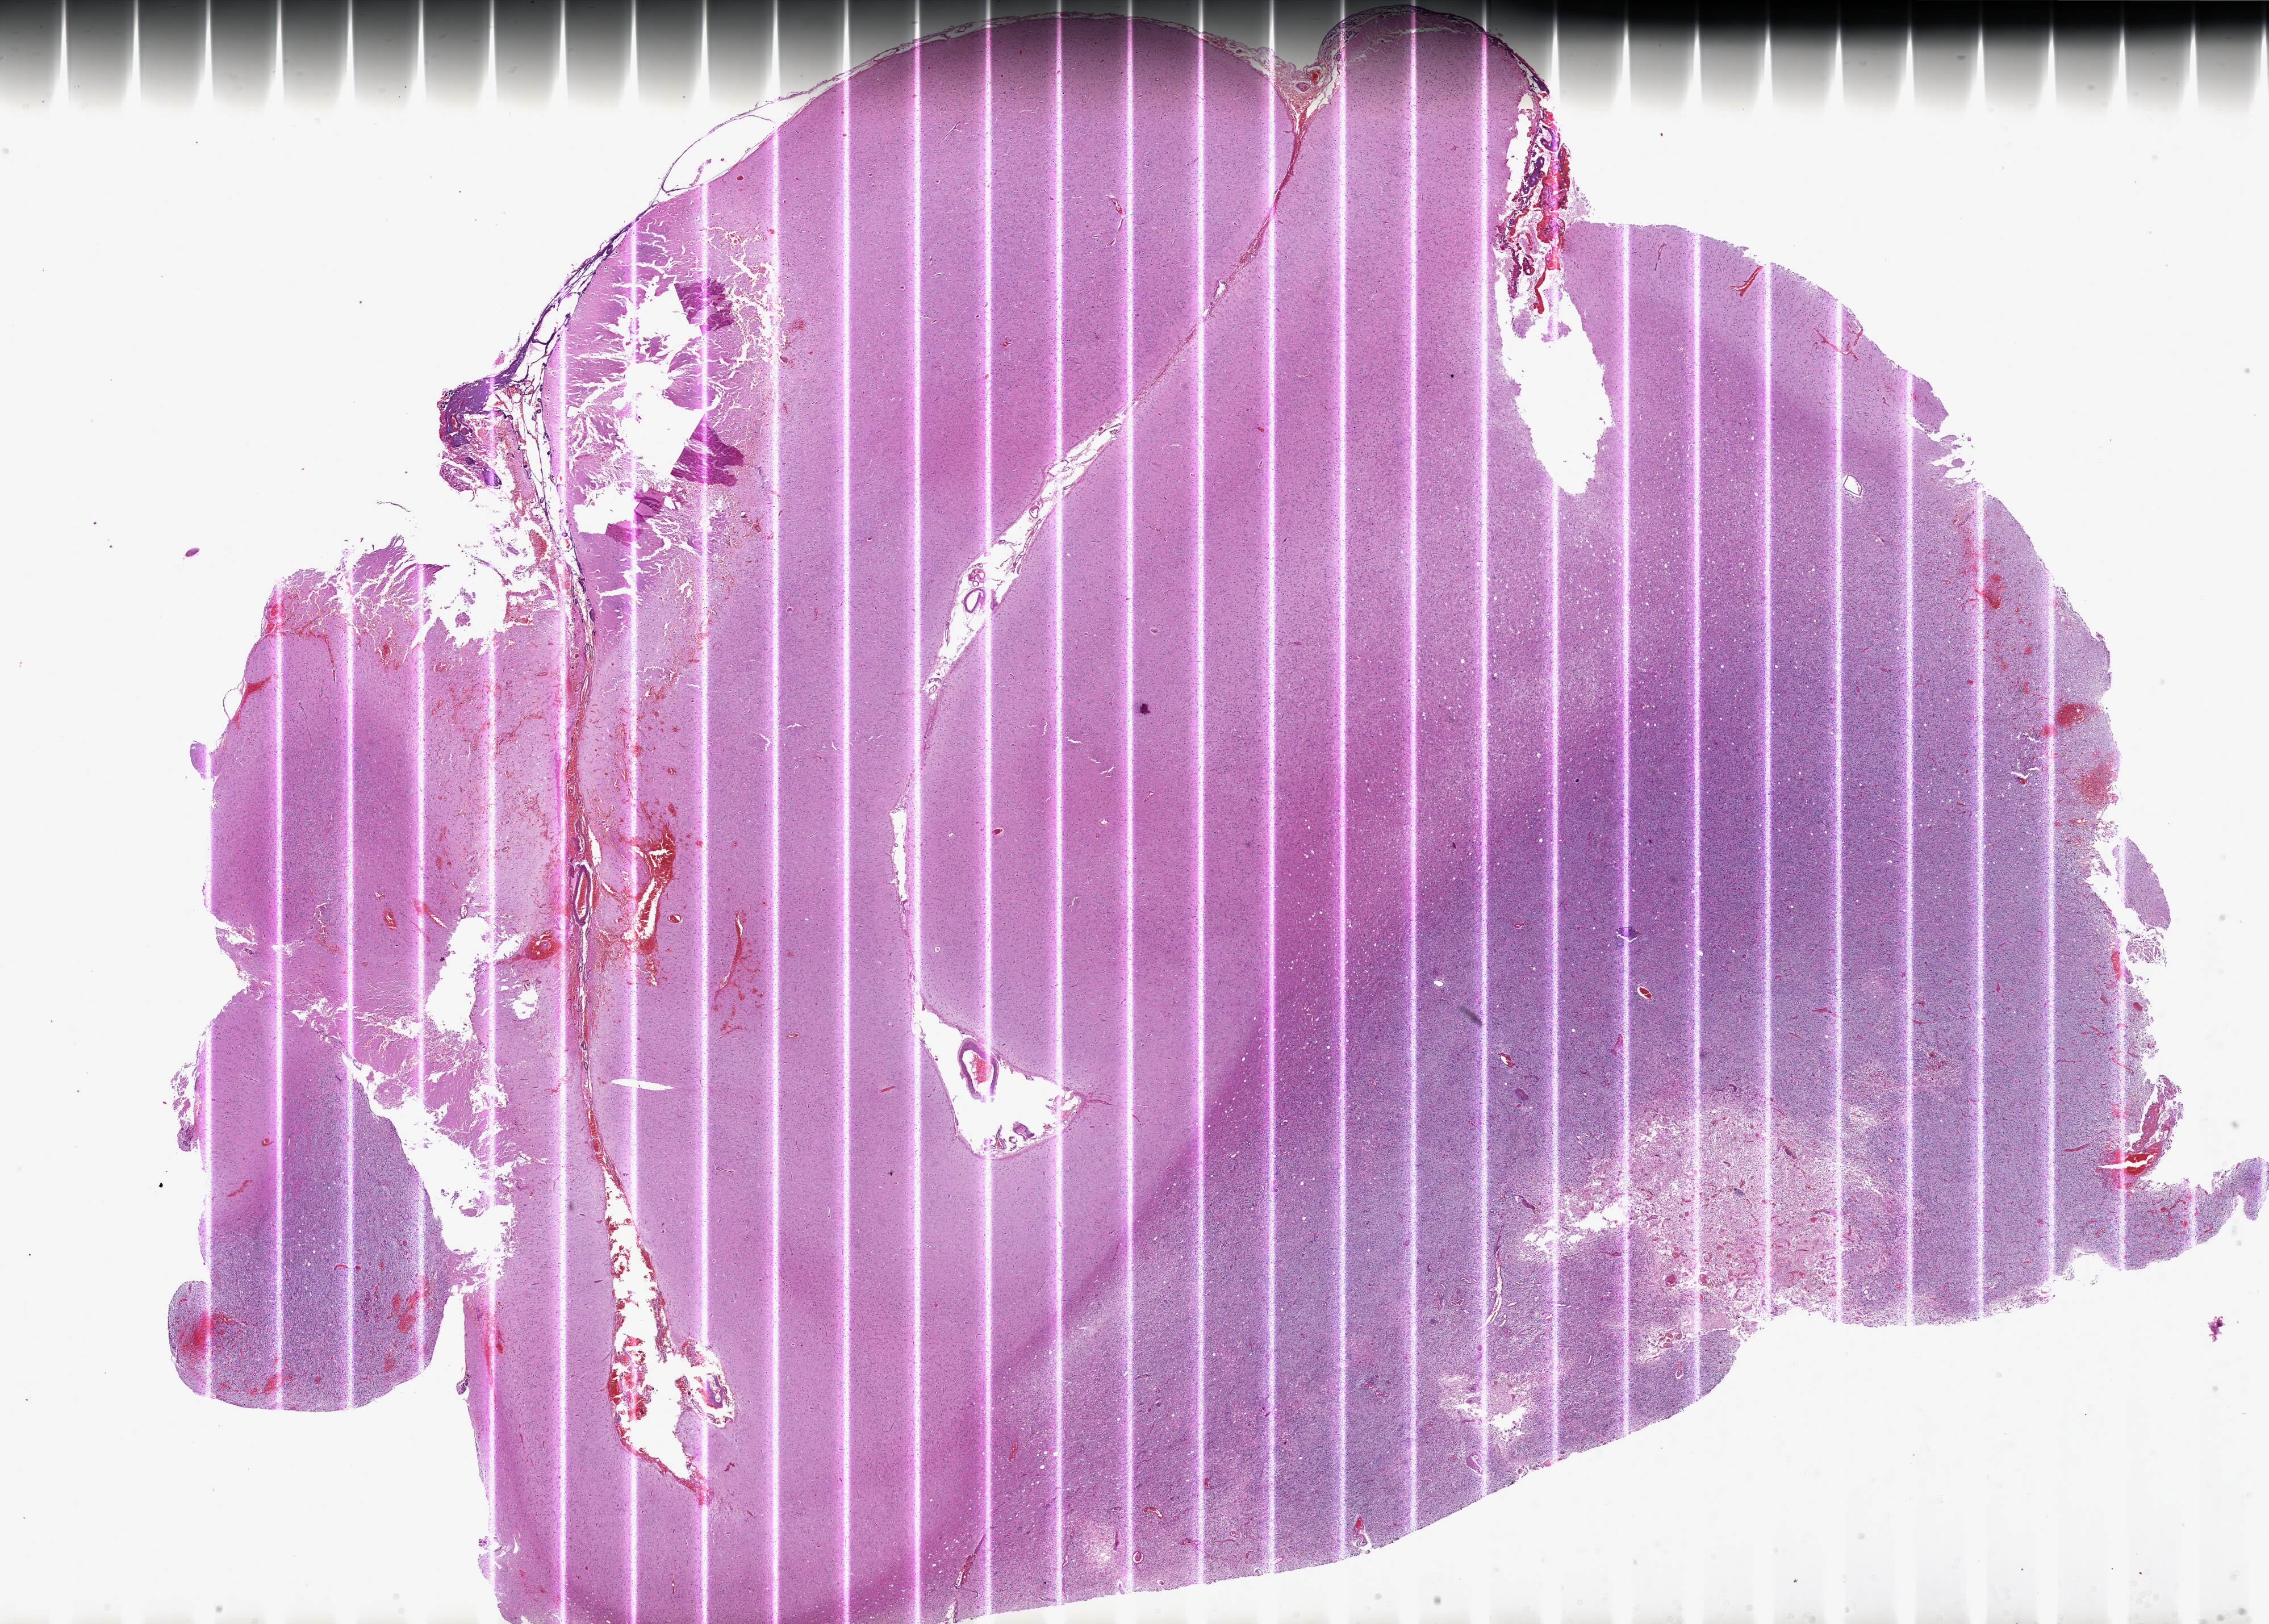
Digitized H&E-stained tissue section (whole slide) — whole scanned area (about 32.0 x 22.9 mm, acquisition: 20x scan) shown as a low-resolution overview. Formalin-fixed paraffin-embedded (FFPE) diagnostic section. Brain, primary tumour sample. Male, age 49 years at initial diagnosis.
Histologic diagnosis: Glioblastoma.